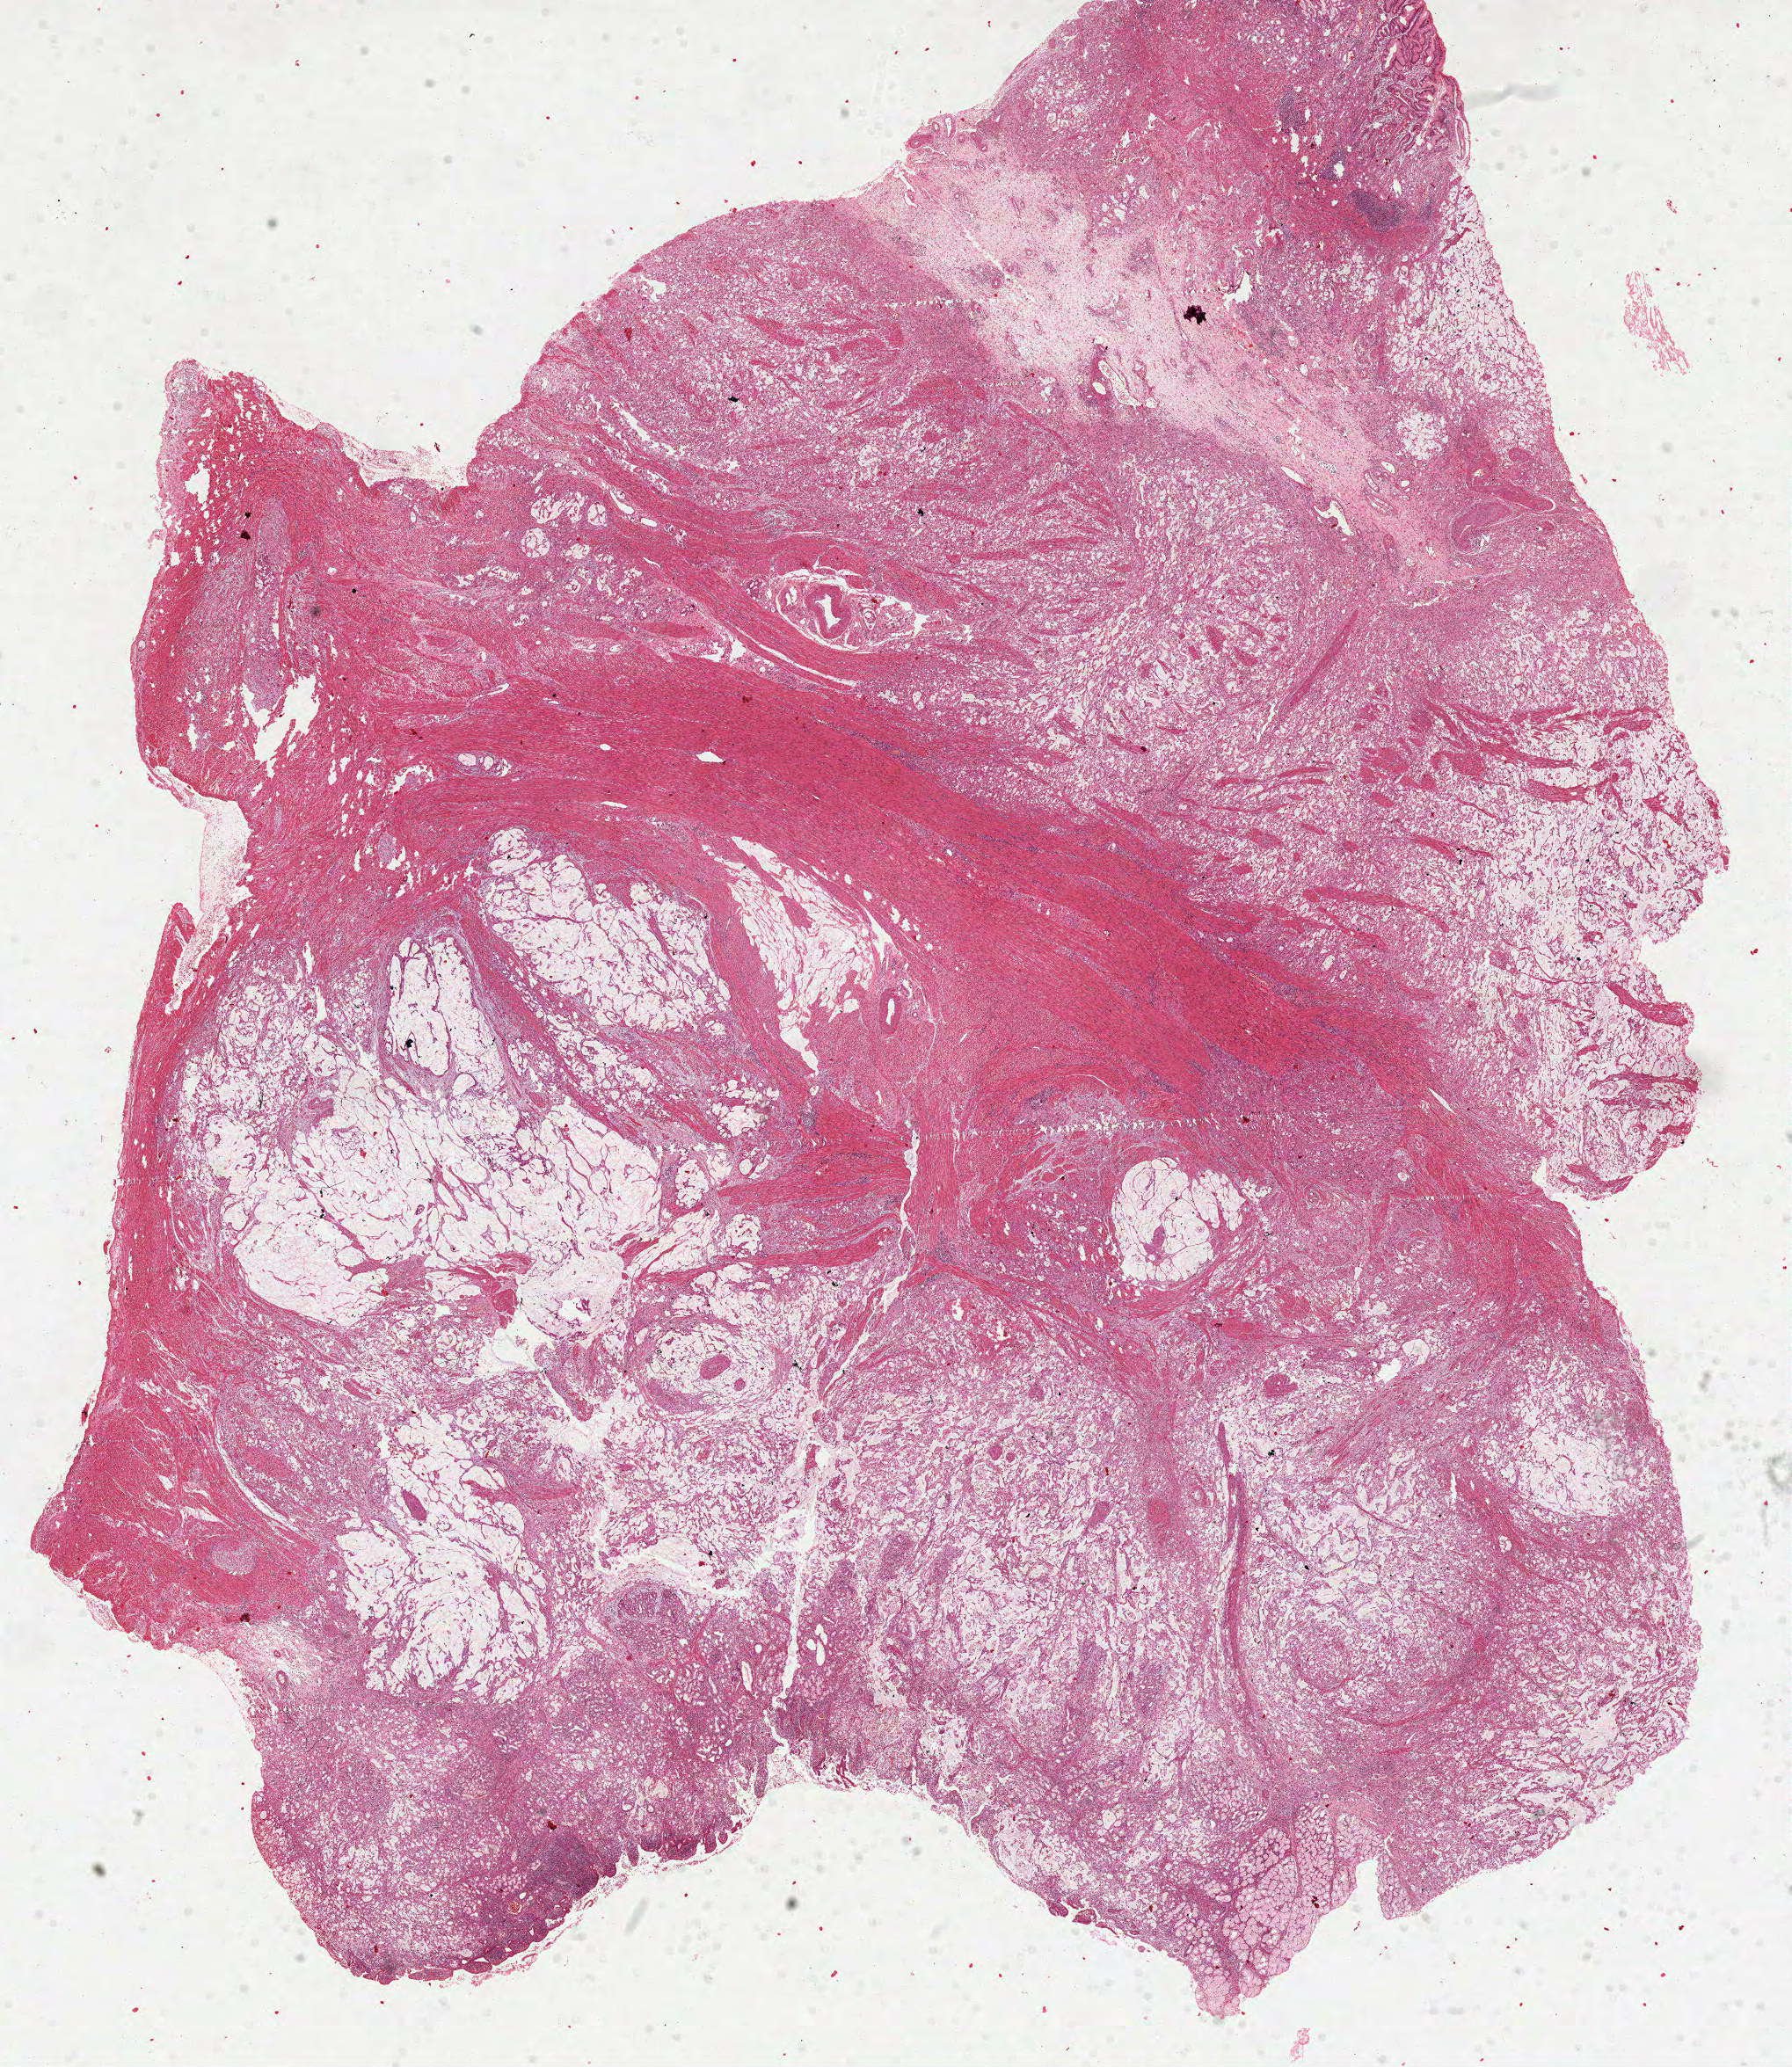
H&E whole-slide image — shown as a low-resolution overview of the whole scanned area (about 16.4 x 19.0 mm), formalin-fixed paraffin-embedded (FFPE) diagnostic section, sample: primary tumour, stomach. Male, age 82 years at initial diagnosis. Histologic grade: G2 (moderately differentiated).
- diagnosis: Mucinous adenocarcinoma (gastric antrum)
- AJCC pathologic stage: II (6th edition)